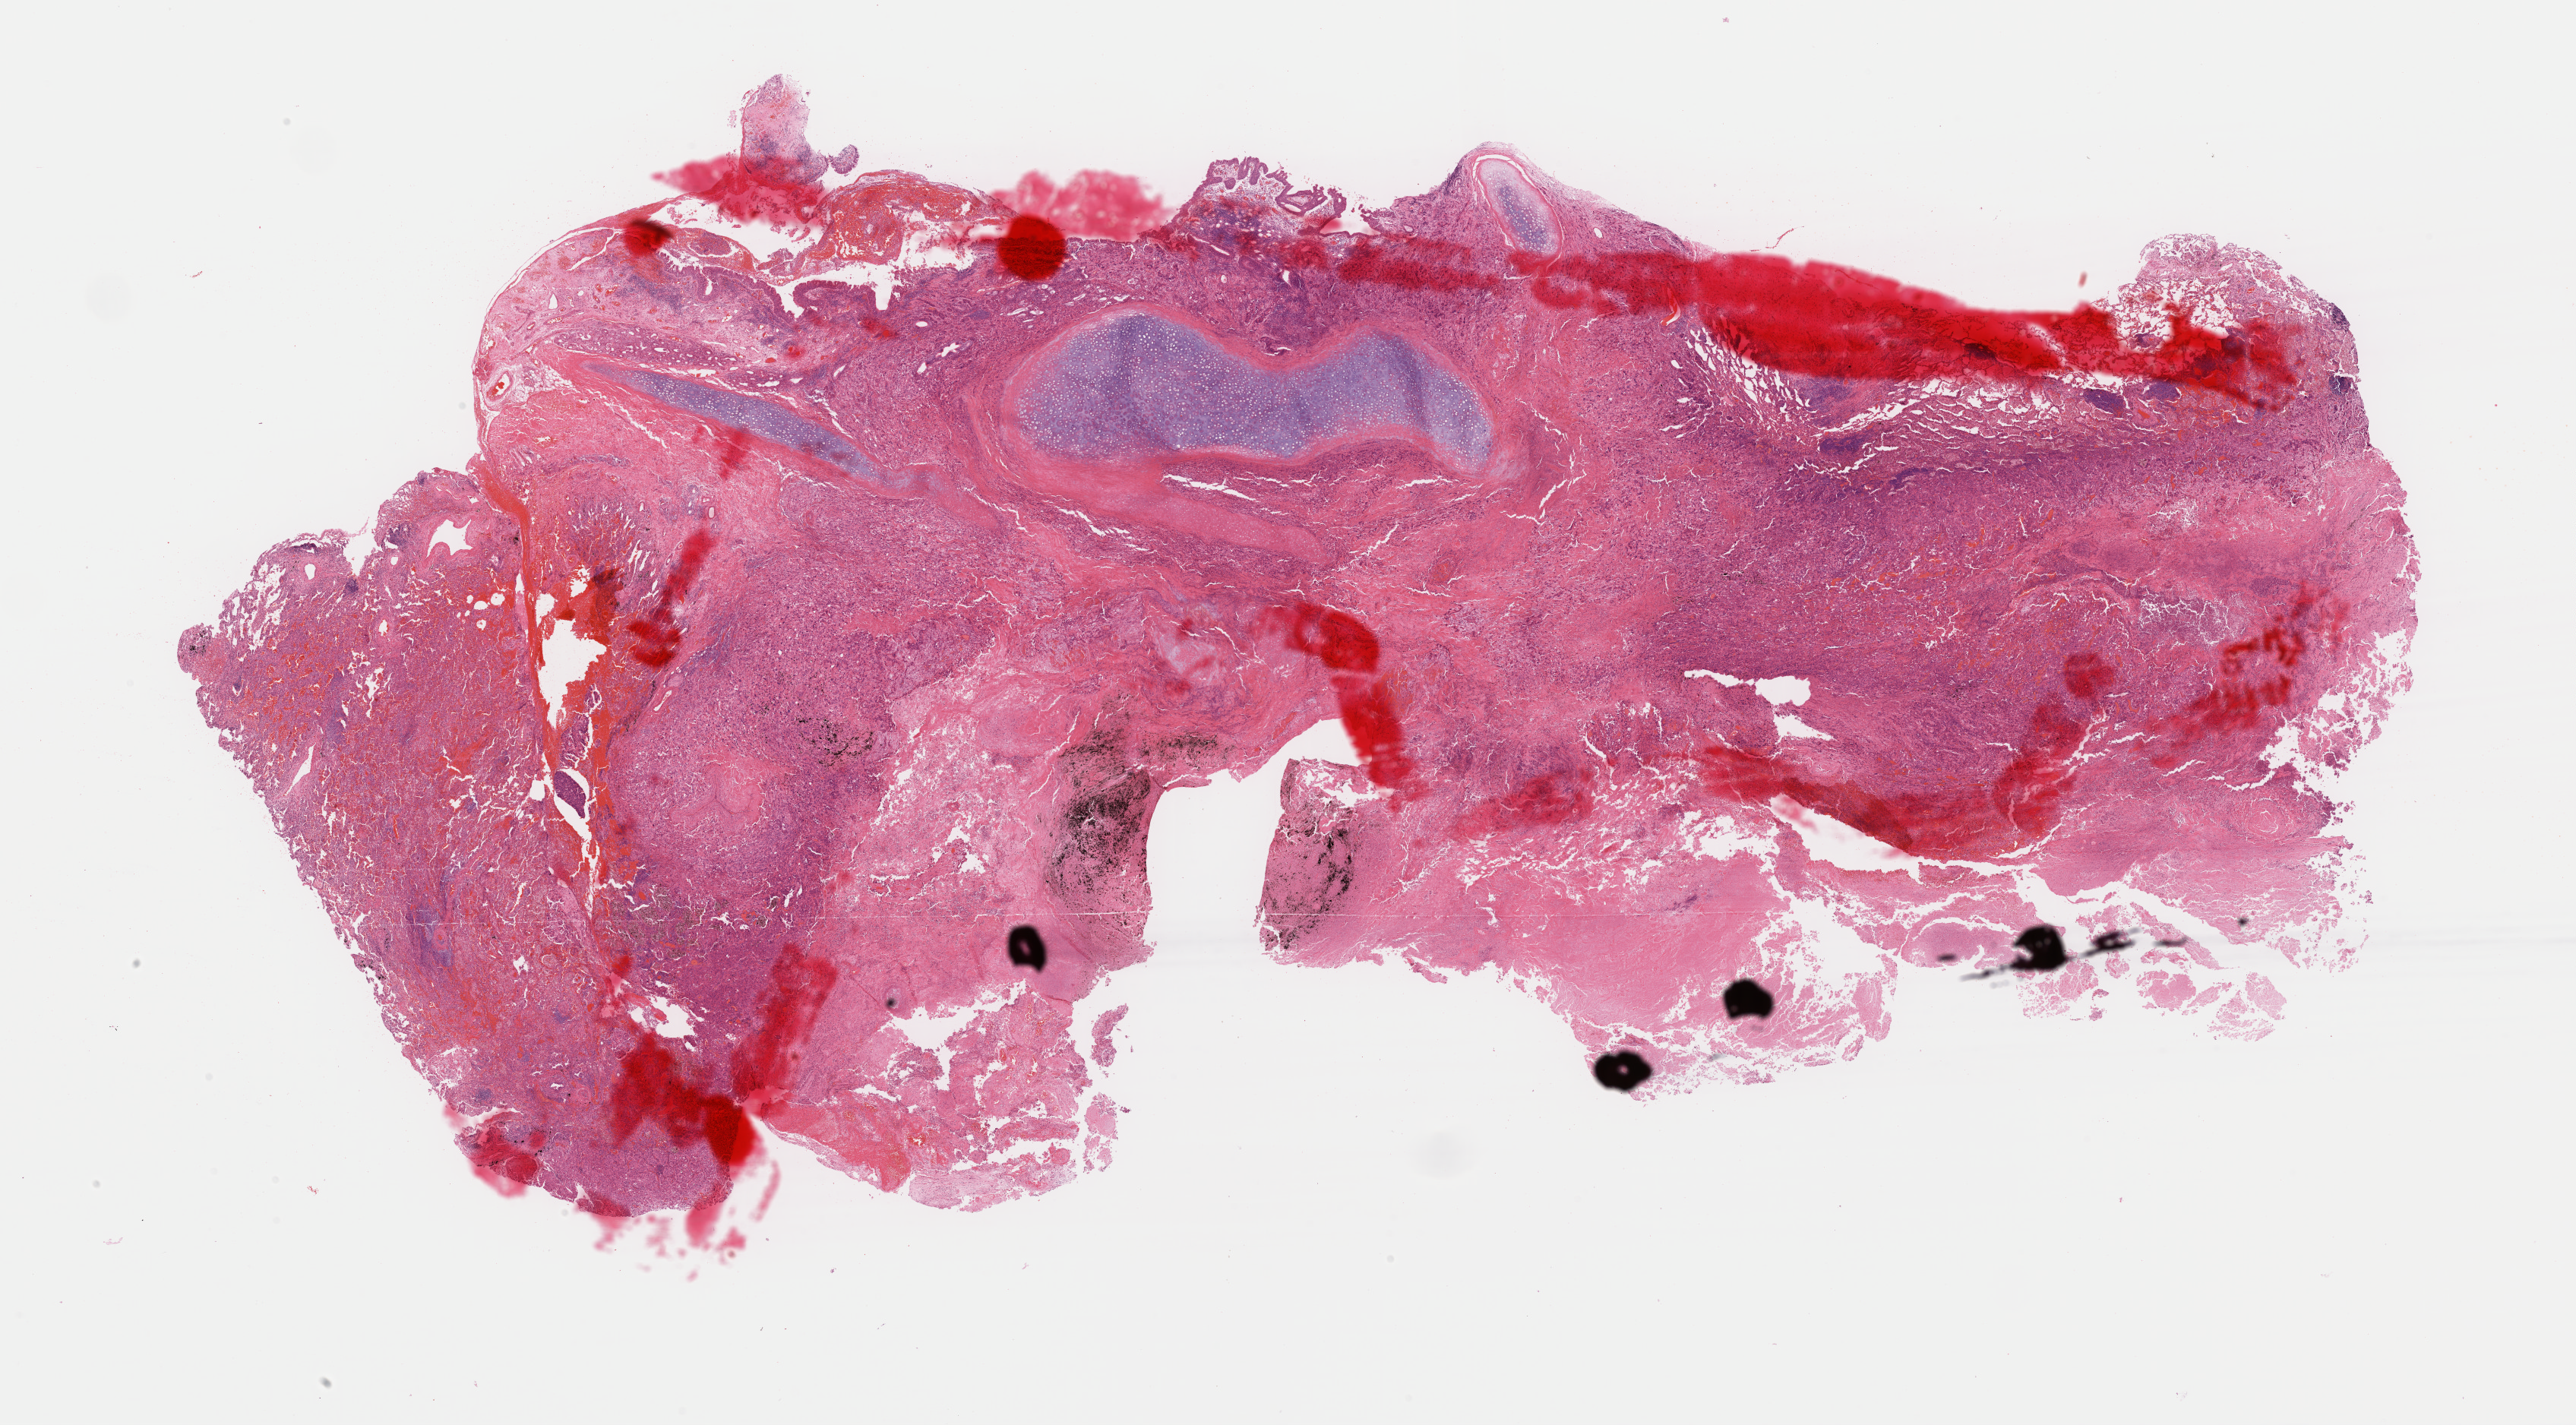
Digitized Hematoxylin and eosin (H&E) stained tissue section (whole slide), low-resolution overview of the scanned area, about 26.8 x 14.8 mm (slide scanned at 40x), FFPE section, sample: primary tumour, lung. Male, age 47 years at initial diagnosis.
Diagnosis: Squamous cell carcinoma, NOS (upper lobe, lung).